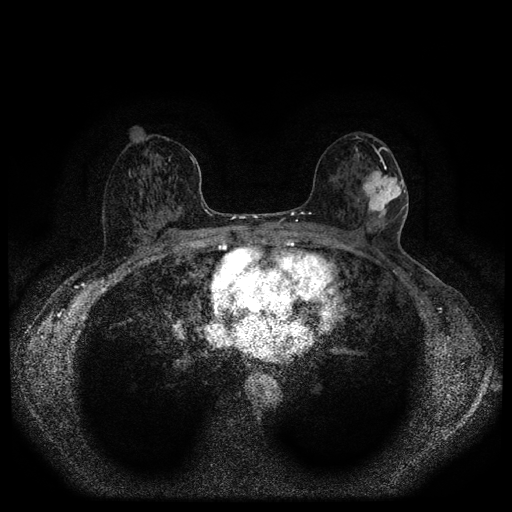
Breast MRI (dynamic contrast-enhanced, multi-phase), one axial slice; slice 57 of 116 in the series (ordered by position); dynamic contrast-enhanced series, time point 2 of 5 at this slice position (early post-contrast); 1.5 T; TE 2.7 ms, TR 5.4 ms; 2 mm slice thickness; 512 × 512 image matrix, field of view 330 × 330 mm. Female patient, age 56 years.
Structures marked on this image (semi-automatic segmentation, software-assisted and operator-edited):
- breast lesion (labelled 'tumour' in the annotation; benign lesions carry a separate 'benign' label): bounding box [x1, y1, x2, y2] px = [362, 167, 405, 225]